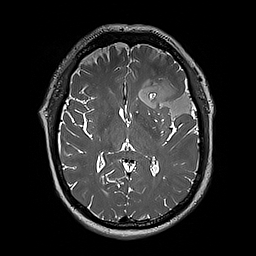
Brain MRI from a brain-tumour surgery series, one axial slice. Position 109 of 192 along the scan axis. 1 mm slice thickness. 256 × 256 image matrix, field of view 250 × 250 mm. From the clinical record (not read from this slice): histopathology: Oligodendroglioma; WHO grade: 3; IDH mutation: yes.
Structures marked on this image (manually delineated by an expert):
- tumour: bounding box (x1, y1, x2, y2) in pixels: (124, 69, 197, 119)